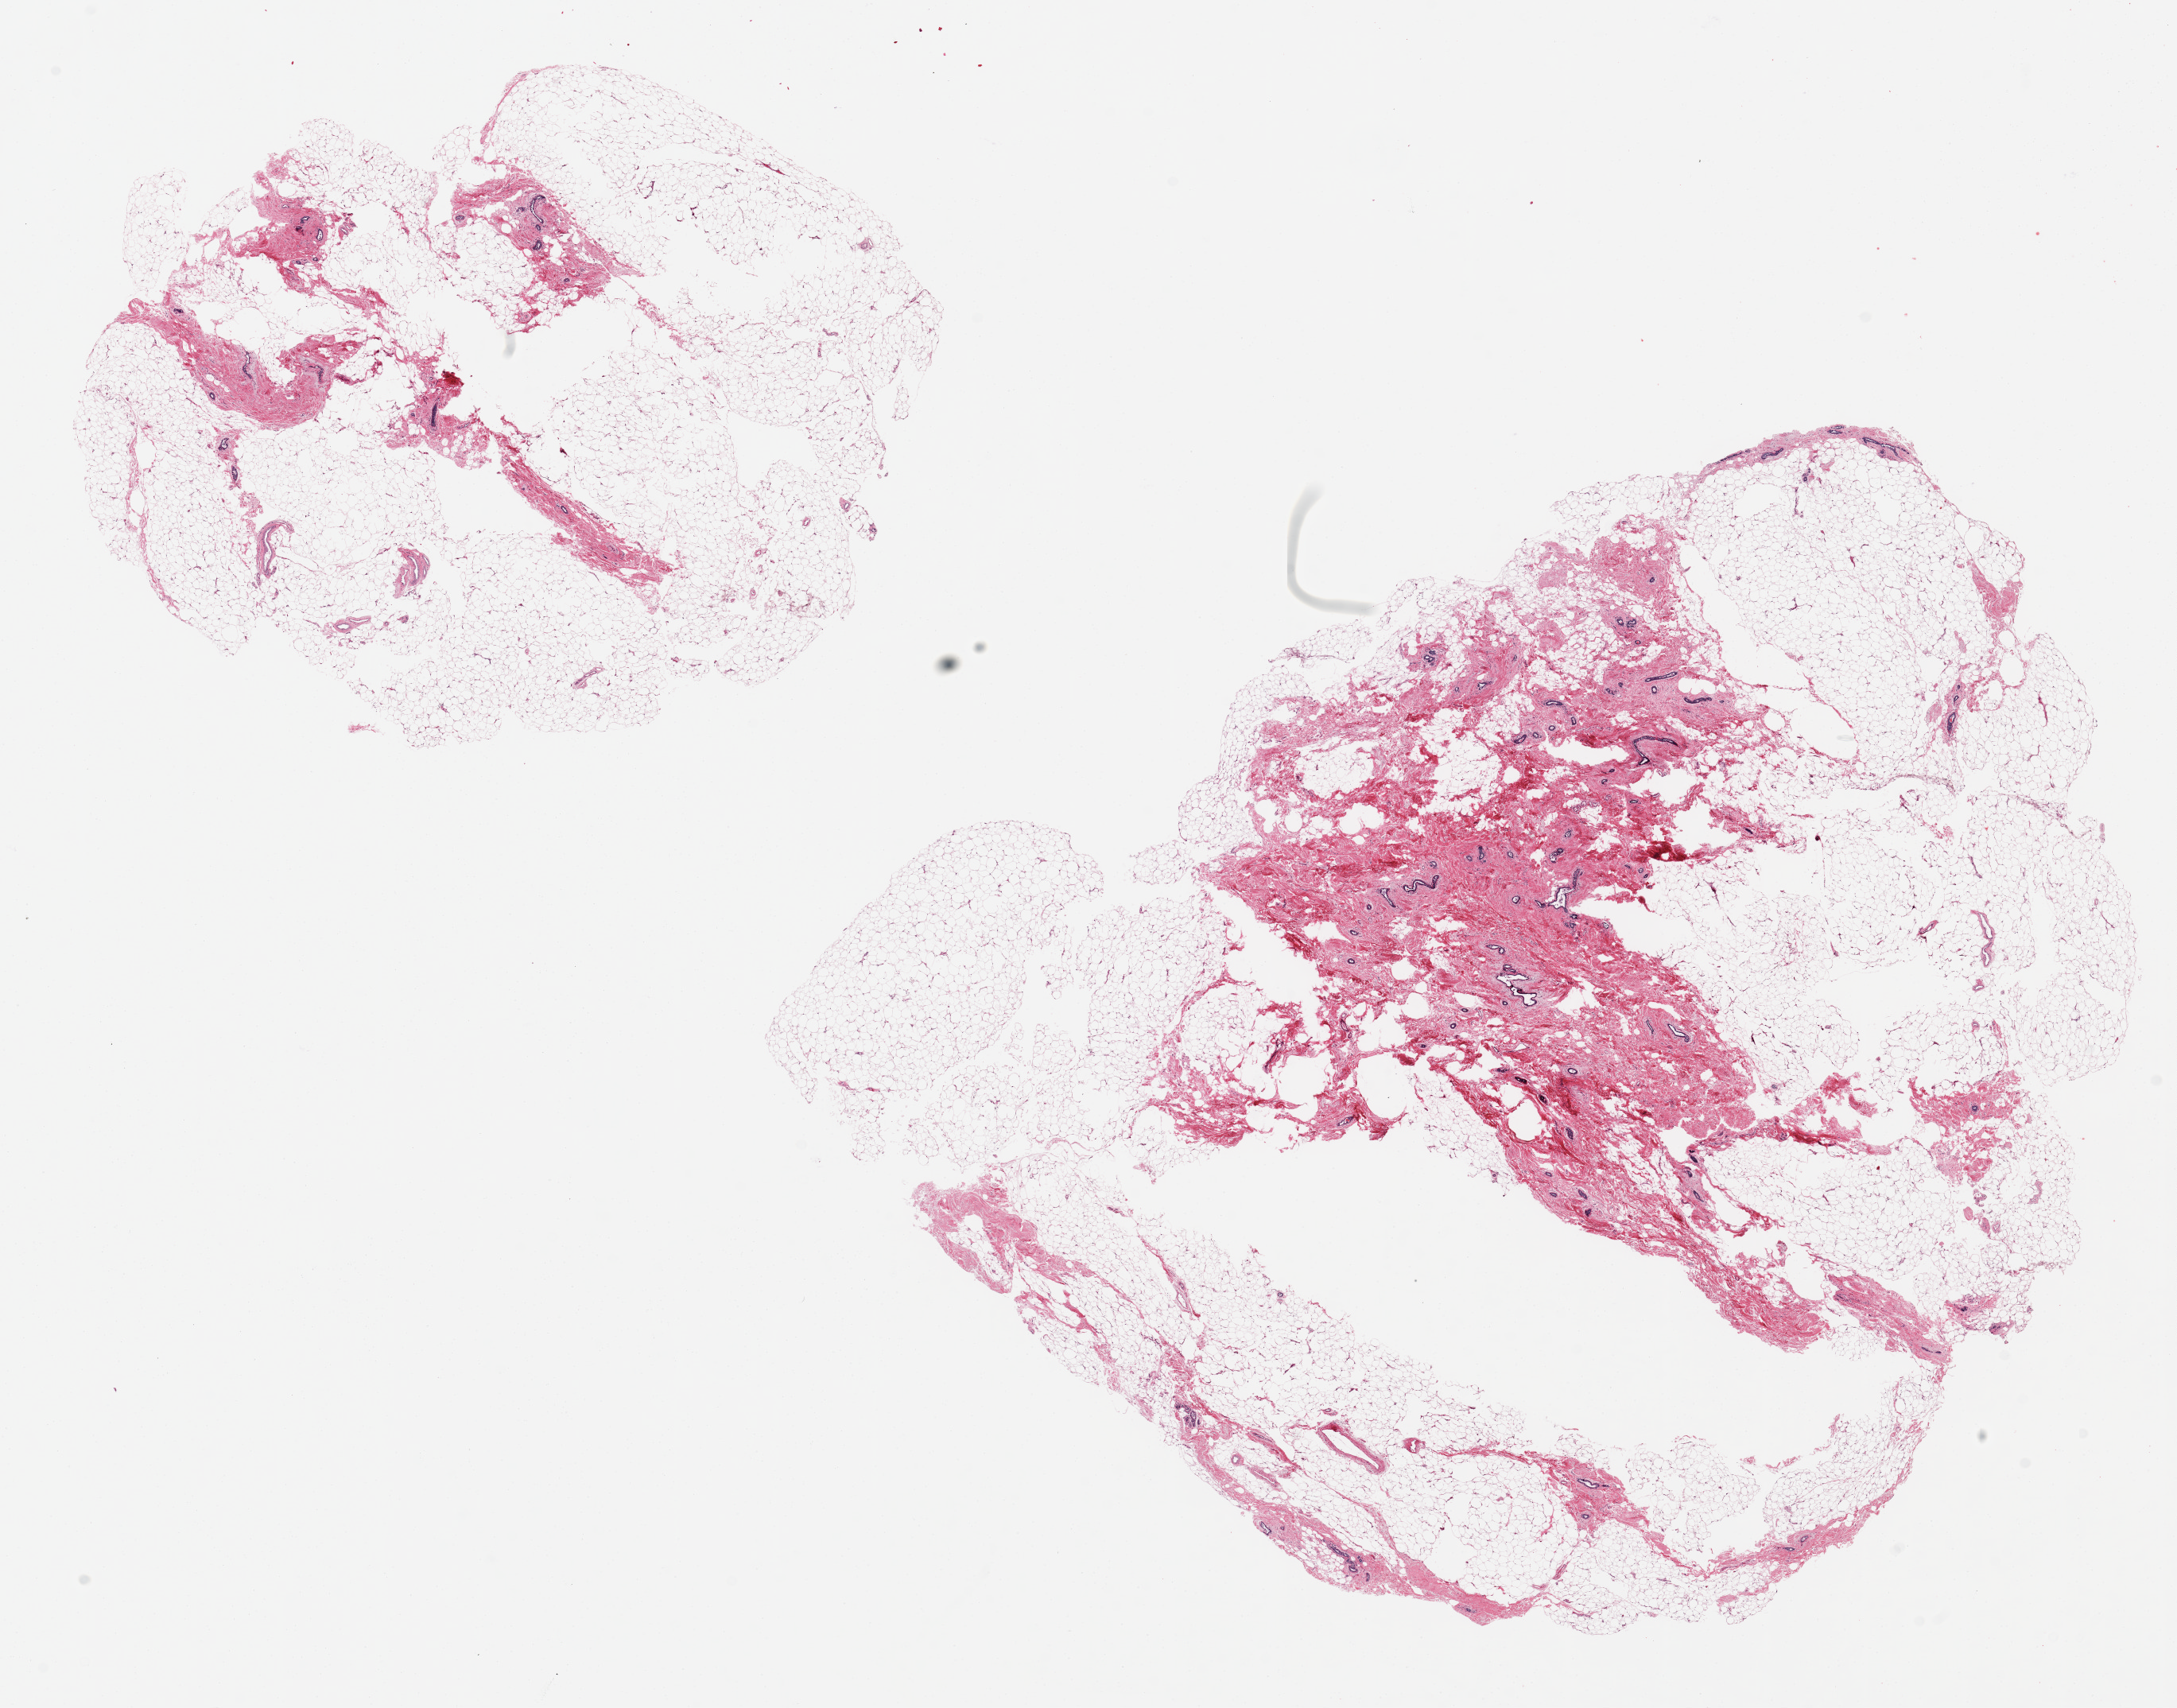
Hematoxylin and eosin (H&E) whole-slide image, low-resolution overview of the scanned area, about 21.7 x 17.0 mm (slide scanned at 20x). PAXgene-fixed, paraffin-embedded tissue. Sampled site (target tissue): breast. Tissue donor sample.
Pathologist's review note for this sample: 2 ~ 10x8mm pieces. Ductal & lobular elements noted, early epithelial sloughing noted.